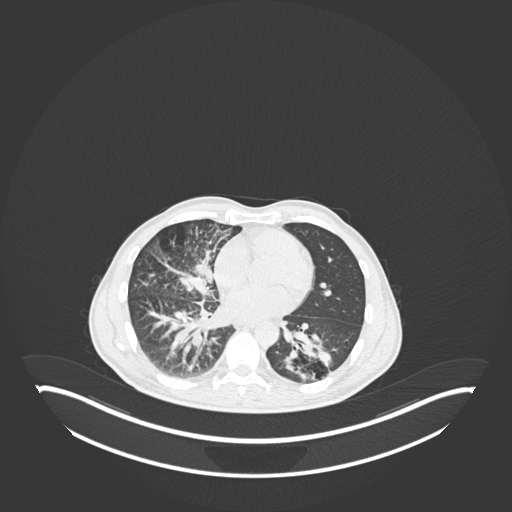
Chest CT, one axial slice. Position 102 of 237 along the scan axis. Lung window (W 1500 / L -600 HU). 1 mm slice thickness. 512 × 512 image matrix. Patient: male, 49 years. Case-level facts recorded for this patient, not image findings: clinical TNM (as recorded): T2b N1 M0.
Annotated regions visible in this slice (bounding box drawn by a radiologist):
- lung tumour (recorded histology: adenocarcinoma): bounding box <279,328,340,383> (left, top, right, bottom; pixels)